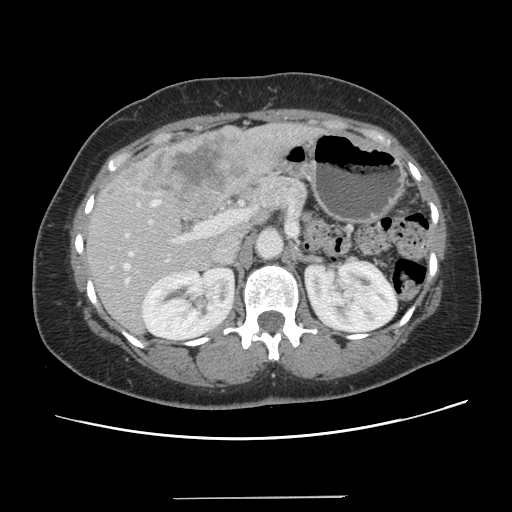
Contrast-enhanced abdominal CT, one axial slice. Slice 71 of 141 in the series (ordered by position). 120 kVp. Soft-tissue window (W 400 / L 40 HU). 512 × 512 image matrix, field of view 366 × 366 mm. Female patient, age 53 years. From the clinical record (not read from this slice): diagnosis: colorectal cancer liver metastases, imaged before liver resection; multiple liver metastases: no; largest metastasis: 14.5 cm; chemotherapy before resection: yes.
Annotated regions visible in this slice (manually delineated by an expert):
- hepatic veins: bounding box (x1, y1, x2, y2) in pixels: (124, 252, 132, 283)
- liver: (88, 124, 314, 332)
- planned liver remnant (the part of the liver to remain after resection): (88, 207, 250, 331)
- portal vein (with intrahepatic branches): (125, 200, 250, 243)
- liver metastasis: (122, 132, 250, 207)